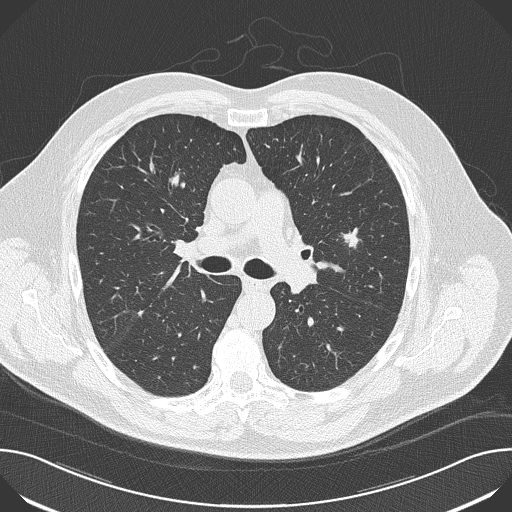
Chest CT (low-dose screening protocol), one axial image; baseline screening round; lung window (W 1500 / L -600 HU); slice 67 of 174 in the series; 512 × 512 image matrix, field of view 380 × 380 mm. Male participant, aged 65 years at enrolment. Former smoker at enrolment.
Expert reader's lesion annotation, bounding box (x1, y1, x2, y2) in pixels: (329, 221, 375, 264). The screening reader recorded 5 non-calcified nodules or masses ≥4 mm on this exam (left upper lobe, left upper lobe, left upper lobe, right upper lobe, right middle lobe); which of them this box marks is not recorded.